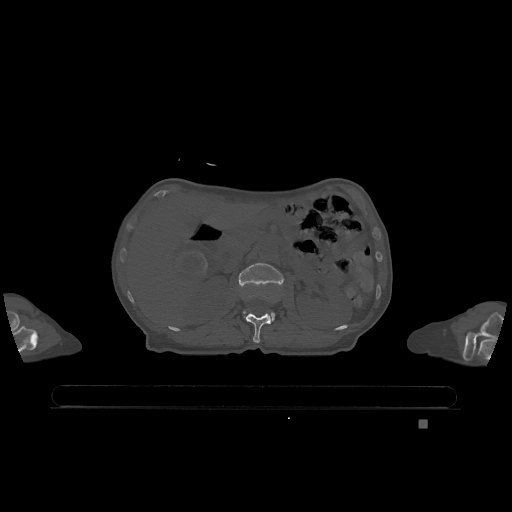
CT including the spine, one axial slice; slice 452 of 1317 in the series (ordered by position); bone window (W 1800 / L 400 HU); 0.5 mm slice thickness; 512 × 512 image matrix, field of view 500 × 500 mm. Patient: female, 74 years. From the clinical record (not read from this slice): primary cancer: lung; vertebrae with lytic lesions (as recorded): T1, T4, T5, T6, L4, L5.
Outlined on this slice (semi-automatic segmentation, software-assisted and operator-edited):
- L1 vertebra: bounding box (x1, y1, x2, y2) in pixels: (245, 313, 271, 343)
- L2 vertebra: (238, 263, 284, 321)